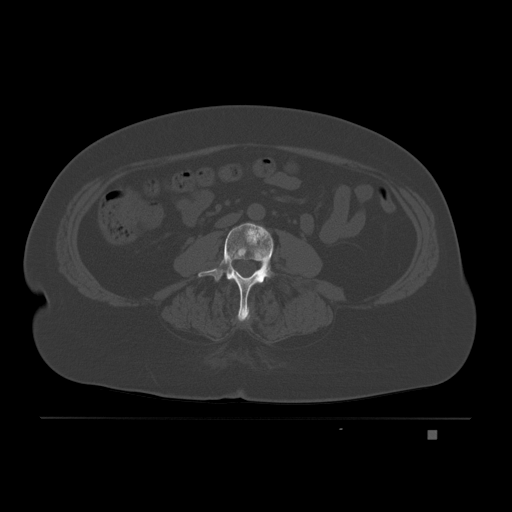
CT including the spine, one axial slice; slice 50 of 221 in the series (ordered by position); bone window (W 1800 / L 400 HU); 3 mm slice thickness; 512 × 512 image matrix. Patient: female, 63 years. Case-level facts recorded for this patient, not image findings: primary cancer: breast.
Annotated regions visible in this slice (semi-automatic segmentation, software-assisted and operator-edited):
- L2 vertebra: bounding box [x1, y1, x2, y2] px = [230, 279, 235, 283]
- L3 vertebra: [198, 222, 274, 321]